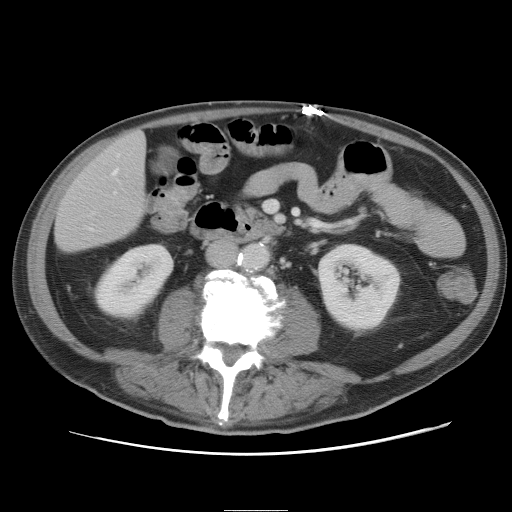
Contrast-enhanced abdominal CT, one axial slice. Slice 12 of 89 in the series (ordered by position). 120 kVp. Intravenous contrast given. Soft-tissue window (W 400 / L 40 HU). 5 mm slice thickness. 512 × 512 image matrix. Male patient, age 69 years. From the clinical record (not read from this slice): diagnosis: colorectal cancer liver metastases, imaged before liver resection; multiple liver metastases: no; largest metastasis: 8.5 cm.
Structures marked on this image (manually delineated by an expert):
- hepatic veins: box from (x=90, y=155) to (x=120, y=230) px
- liver: (x=57, y=132)–(x=147, y=253)
- planned liver remnant (the part of the liver to remain after resection): (x=56, y=132)–(x=146, y=253)